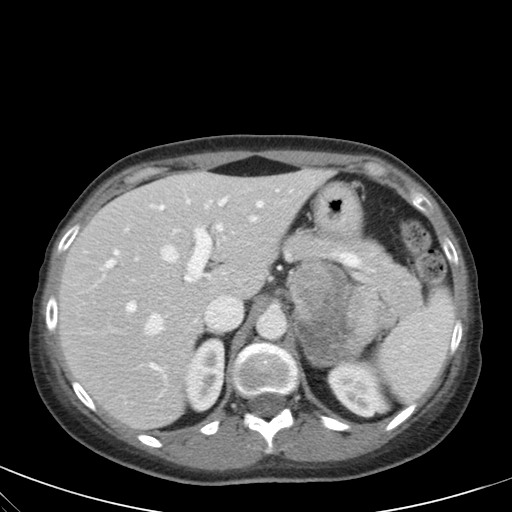
Contrast-enhanced abdominal CT, one axial slice; position 41 of 59 along the scan axis; intravenous contrast given; soft-tissue window (W 400 / L 40 HU); 4 mm slice thickness; 512 × 512 image matrix, field of view 350 × 350 mm. Female patient, age 28 years. Case-level facts recorded for this patient, not image findings: diagnosis: adrenocortical carcinoma; tumour side: left adrenal; tumour size at pathology: 7 cm; Ki-67 index: 40 %; stage (as recorded): 4.
Annotated regions visible in this slice (semi-automatic segmentation, software-assisted and operator-edited):
- mass: bounding box <291,263,396,364> (left, top, right, bottom; pixels)